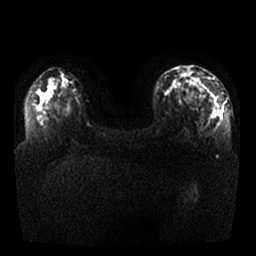
Breast MRI, one axial slice. Position 10 of 25 along the scan axis. Diffusion-weighted series; image 2 of 4 stored at this slice position (different b-values; order by instance number). 1.5 T. 4 mm slice thickness. 256 × 256 image matrix, field of view 340 × 340 mm. Female patient.
Annotated regions visible in this slice (outlined manually by an expert reader):
- tumour on diffusion-weighted imaging: bounding box <179,68,204,87> (left, top, right, bottom; pixels)